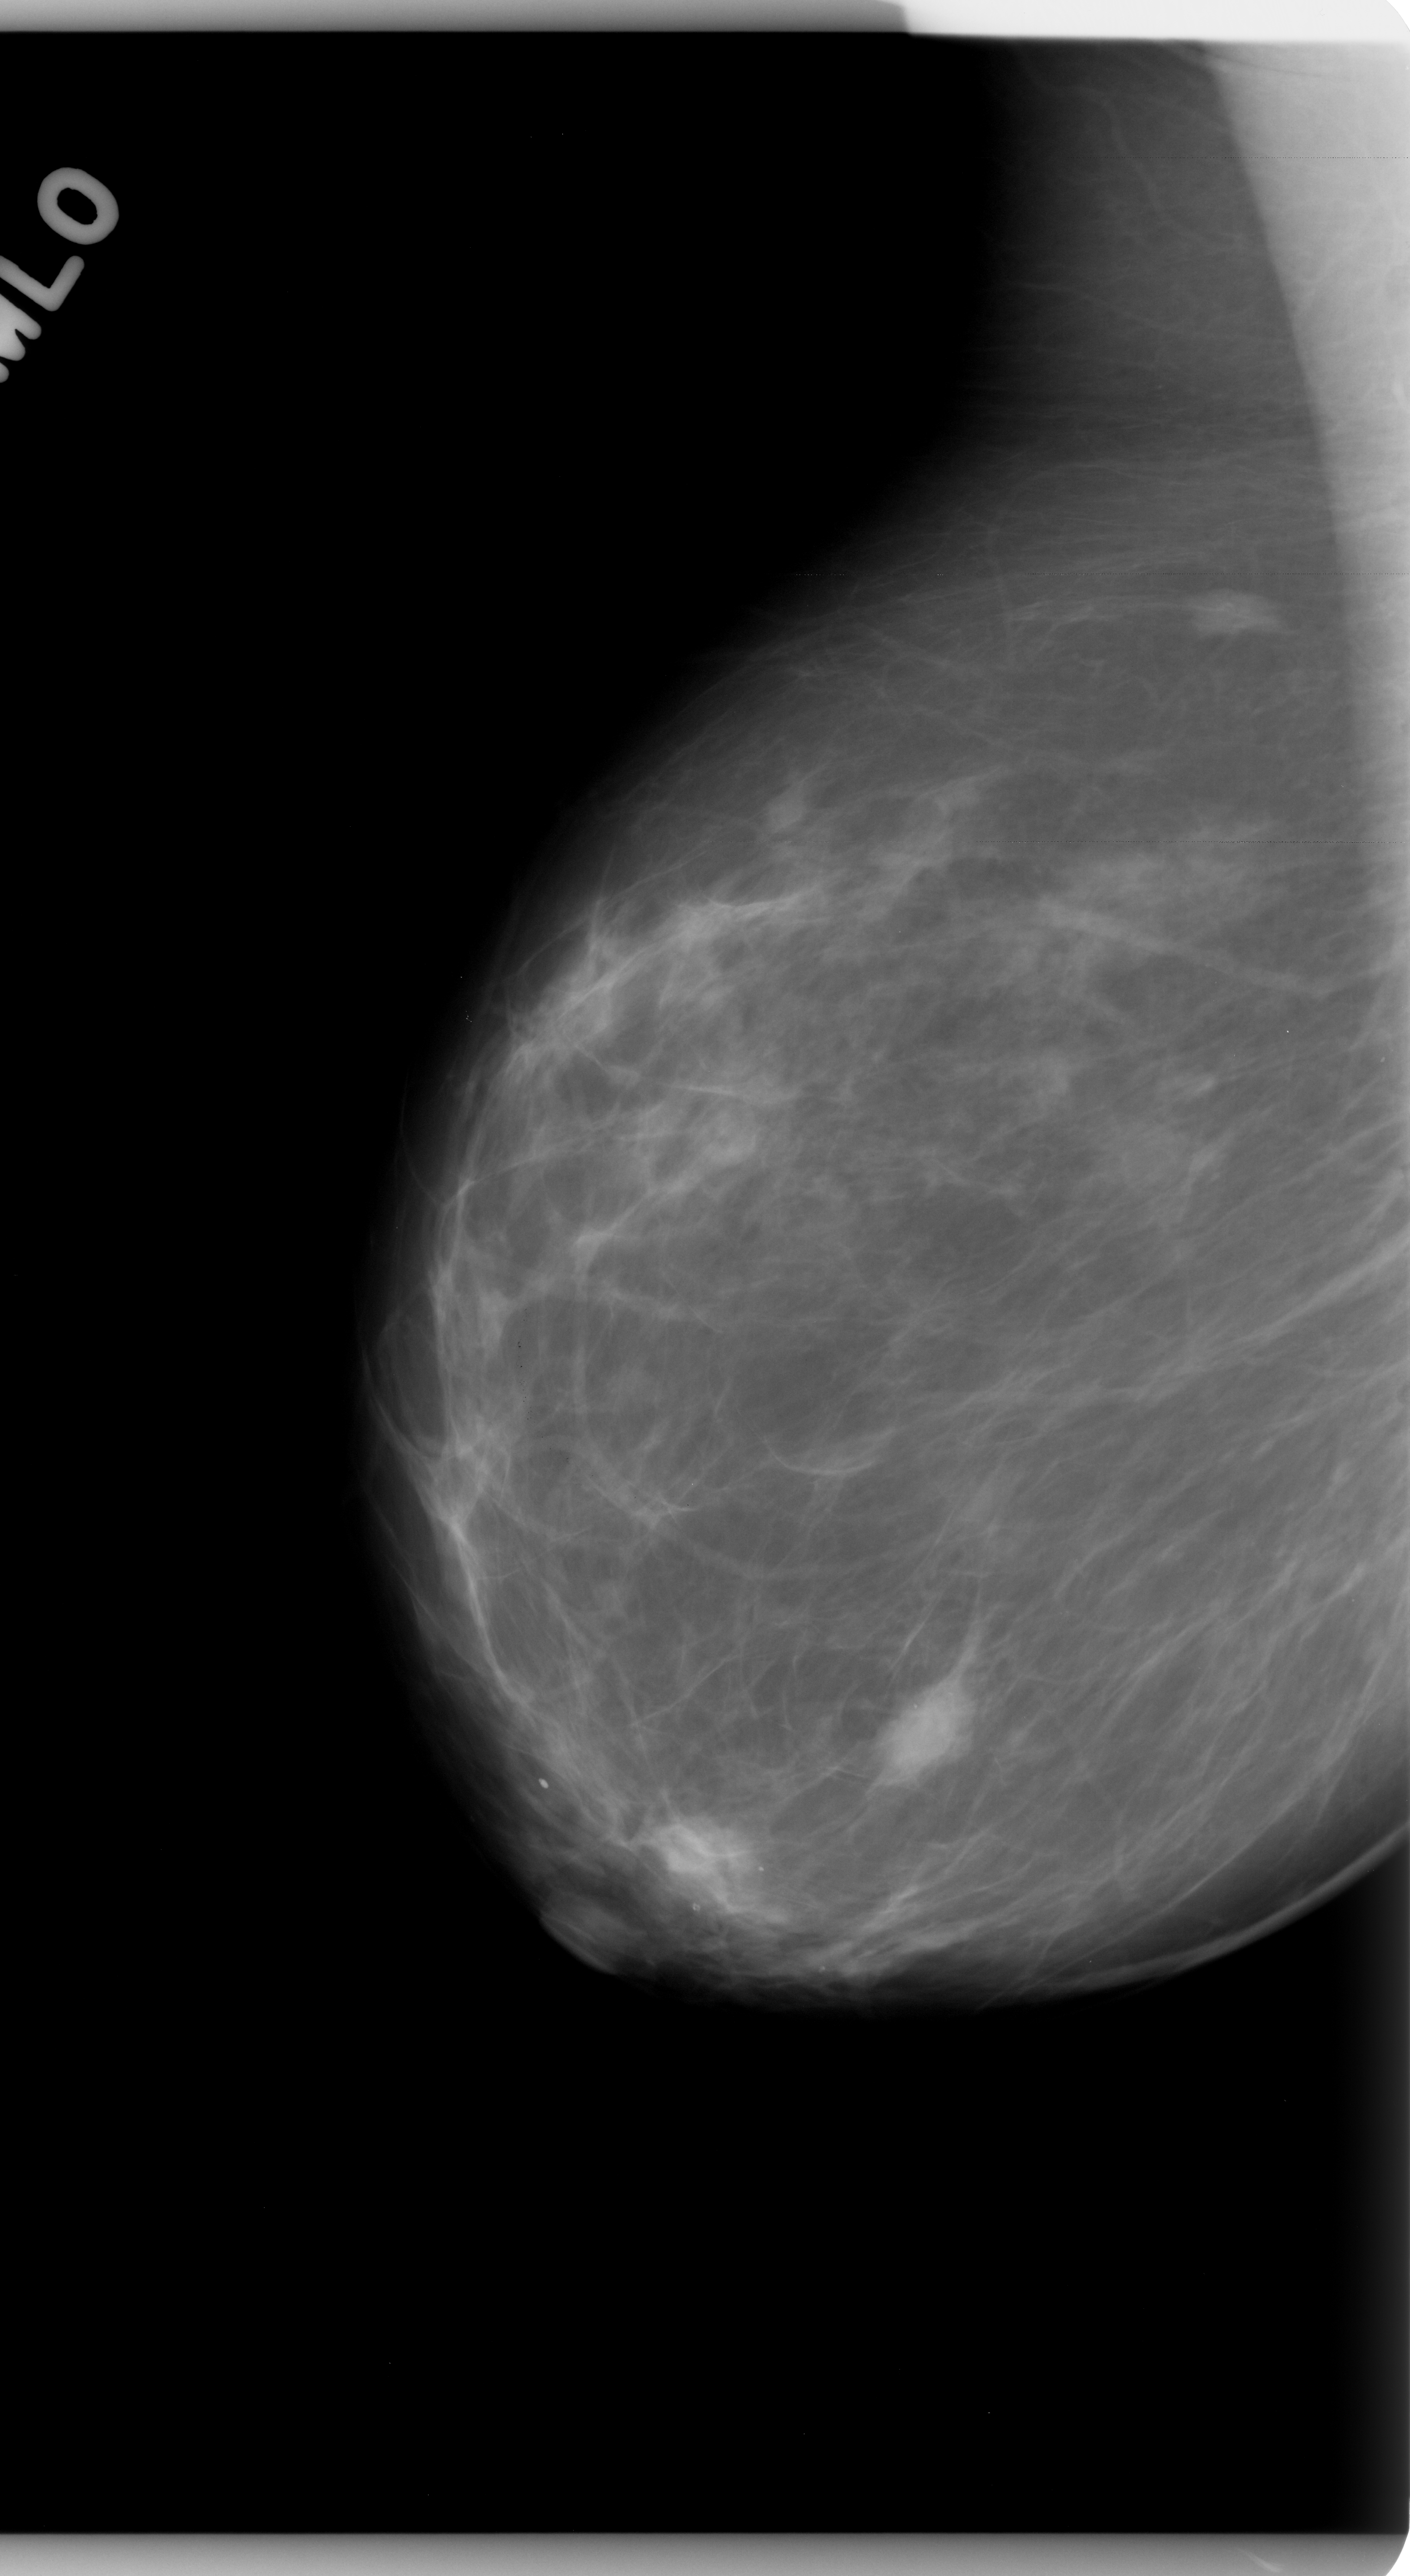
Digitized screen-film mammogram; right breast; mediolateral oblique (MLO) view; BI-RADS breast density category 1 (scale 1–4).
Radiologist-marked abnormalities on this image: mass, shape oval, margins microlobulated; BI-RADS assessment category 4; subtlety rating 5 on a 1 (subtle) to 5 (obvious) scale; pathology (as recorded): malignant.